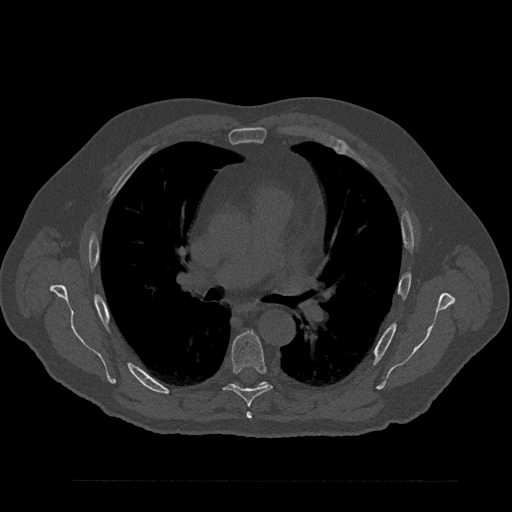
CT including the spine, one axial slice; position 552 of 797 along the scan axis; 120 kVp; bone window (W 1800 / L 400 HU); 0.5 mm slice thickness; 512 × 512 image matrix, field of view 430 × 430 mm. Patient: male, 61 years. Case-level facts recorded for this patient, not image findings: primary cancer: prostate.
Structures marked on this image (semi-automatically segmented with operator editing):
- T5 vertebra: bounding box <246,412,252,419> (left, top, right, bottom; pixels)
- T6 vertebra: <224,331,272,407>
- T7 vertebra: <236,381,267,386>